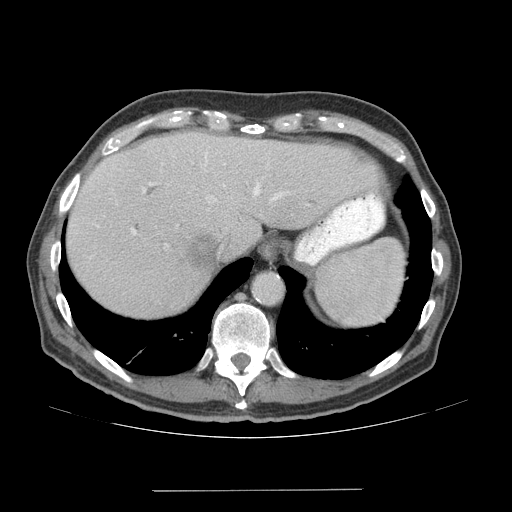
Contrast-enhanced abdominal CT (liver protocol), one axial slice; slice 55 of 77 in the series (ordered by position); soft-tissue window (W 400 / L 40 HU); 2.5 mm slice thickness; 512 × 512 image matrix, field of view 400 × 400 mm. From the clinical record (not read from this slice): diagnosis: hepatocellular carcinoma (patient treated with transarterial chemoembolisation; whether this scan precedes or follows treatment is not stated here); TNM stage (as recorded): Stage-IVA; Child-Pugh class: A; tumour differentiation: well differentiated; tumour nodularity: uninodular.
Outlined on this slice (semi-automatically segmented with operator editing):
- liver parenchyma outside the tumour (the mass and vessels are separate outlines, so this box may not span the whole liver): bounding box [x1, y1, x2, y2] px = [66, 132, 378, 318]
- mass: [186, 234, 218, 270]
- liver vessels: [96, 146, 285, 245]